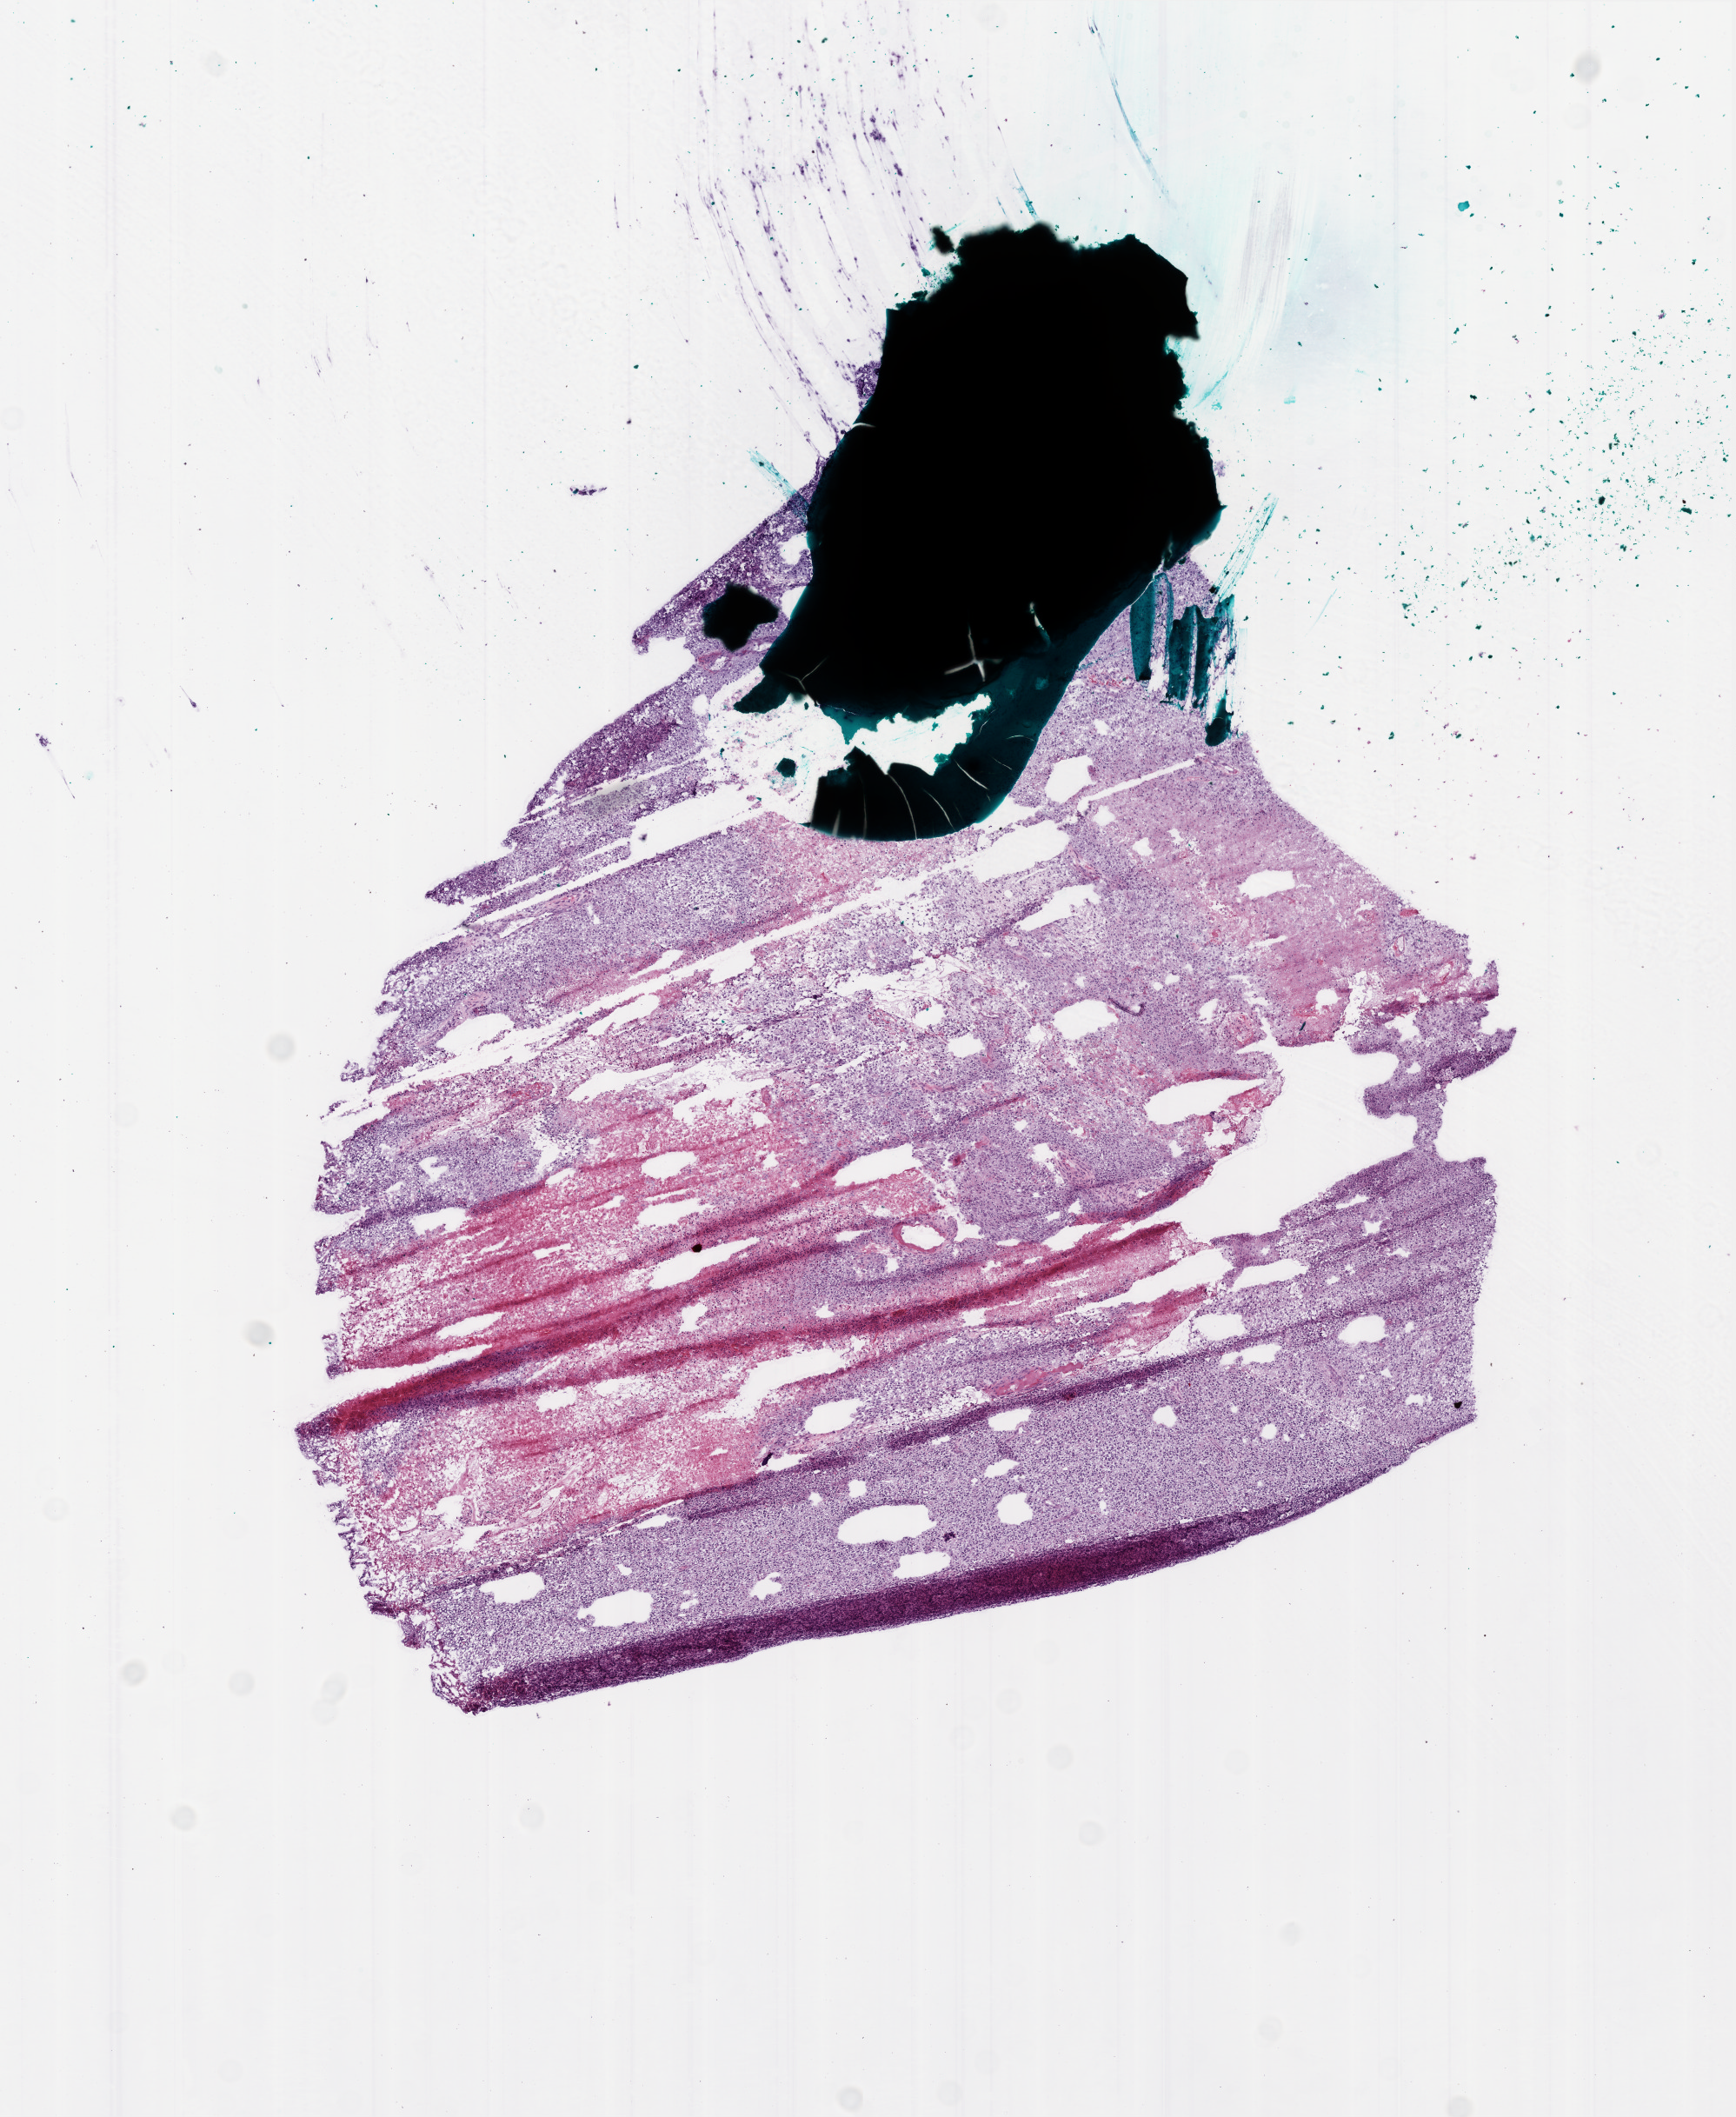
Whole-slide histology image, H&E, a low-resolution overview of the entire scanned area, about 8.0 x 9.7 mm (slide scanned at 20x), frozen section from the bottom of the tissue portion, brain, primary tumour sample. Male, age 74 years at initial diagnosis. Pathologist review of this section (percent, as recorded): tumour cells 60%, tumour nuclei 95%, normal cells 0%, stromal cells 0%, necrosis 40%.
Diagnosis: Glioblastoma.